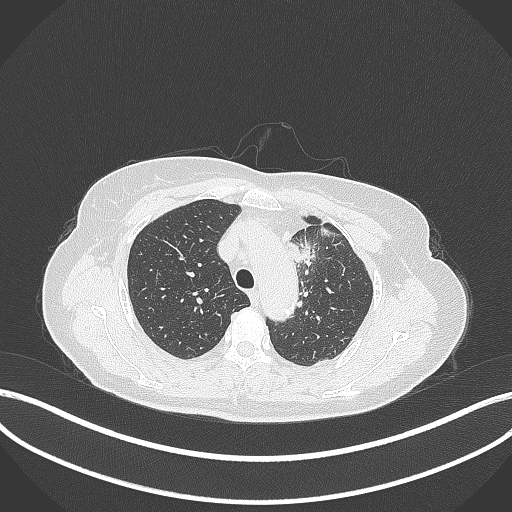
Chest CT, one axial slice; position 256 of 369 along the scan axis; reconstruction kernel B70f; lung window (W 1500 / L -600 HU); 1 mm slice thickness; 512 × 512 image matrix, field of view 400 × 400 mm. Patient: female, 65 years. From the clinical record (not read from this slice): clinical TNM (as recorded): T2a N0 M0; histopathological grade: G2-3.
Outlined on this slice (bounding box drawn by a radiologist):
- lung tumour (recorded histology: adenocarcinoma): bounding box <287,236,316,267> (left, top, right, bottom; pixels)